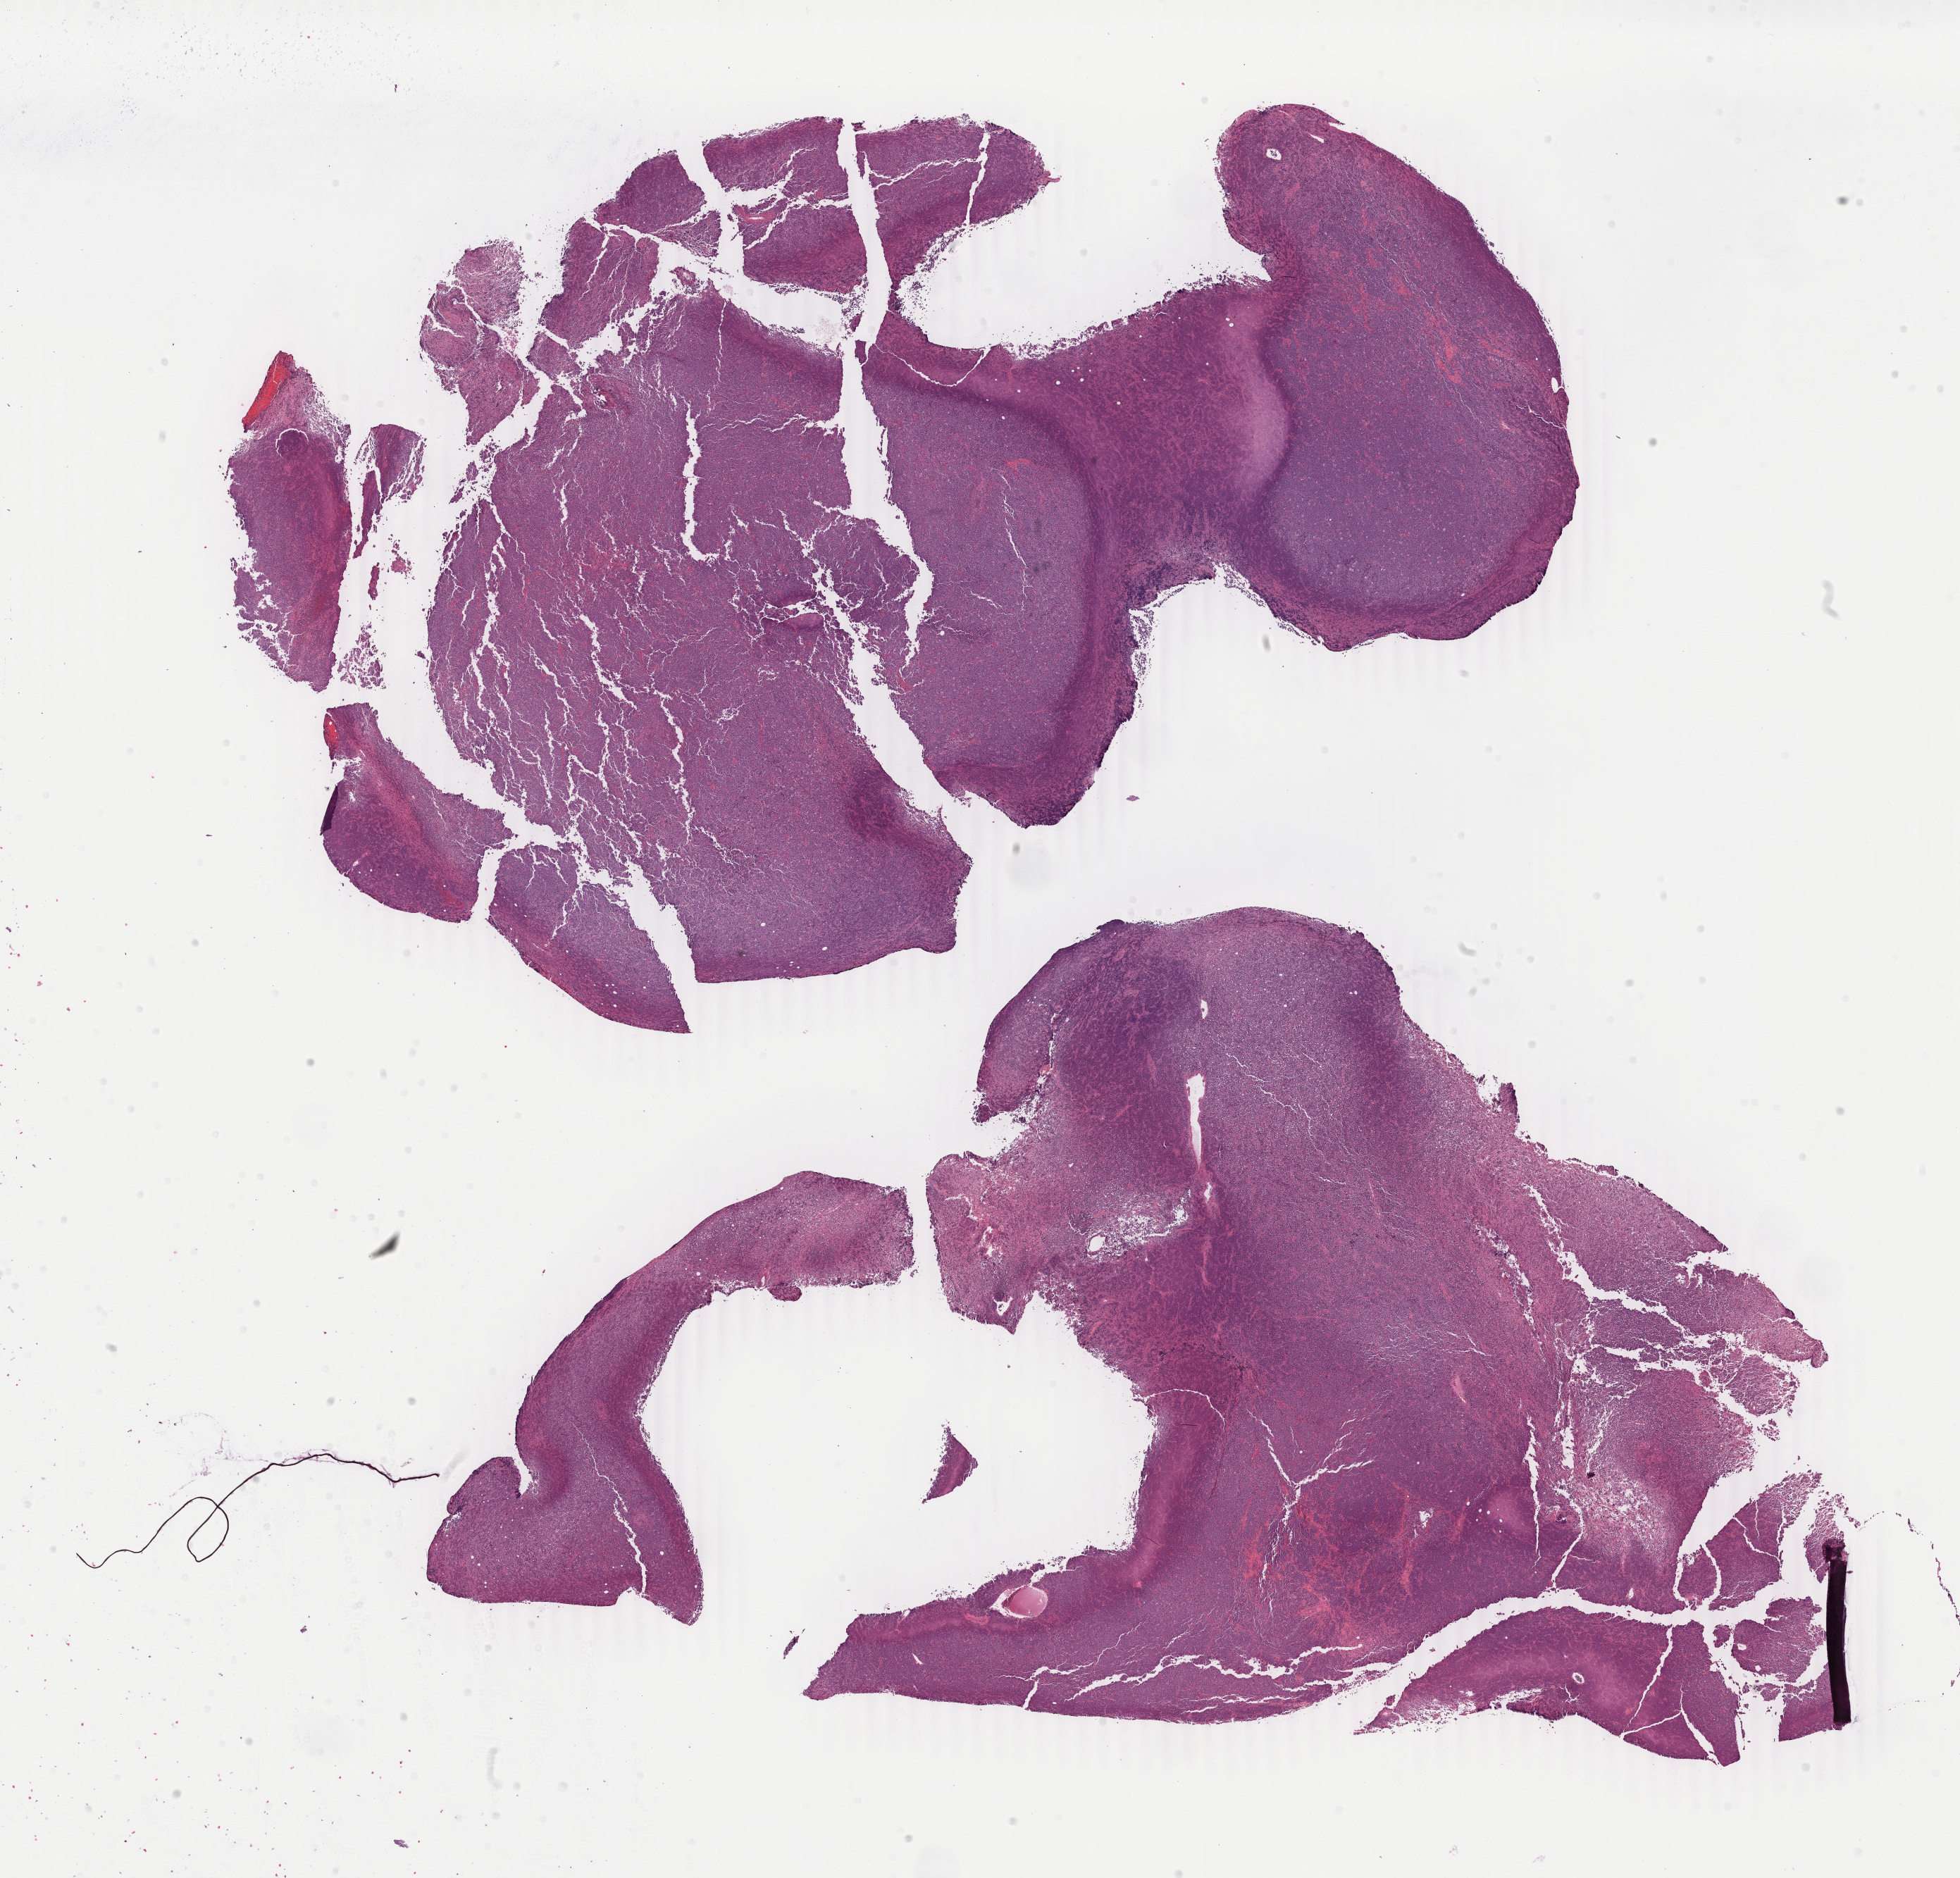
Digitized hematoxylin and eosin (H&E)-stained section, a low-resolution overview of the entire scanned area, about 22.1 x 21.2 mm. Tumor tissue. Site: liver. Male patient, 45 years old.
Histologic diagnosis: Diffuse large B-cell lymphoma, NOS.